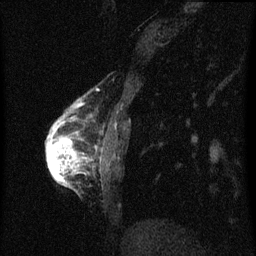
Breast MRI (dynamic contrast-enhanced), one sagittal slice. Position 13 of 60 along the scan axis. Dynamic contrast-enhanced series, image 2 of 3 at this slice position (ordered by acquisition). 1.5 T. TE 4.2 ms, TR 8 ms. 2 mm slice thickness. 256 × 256 image matrix, field of view 180 × 180 mm. Patient: female, 56 years.
Structures marked on this image (semi-automatic segmentation, software-assisted and operator-edited):
- analysis volume of interest (the breast-tissue region the enhancement analysis was run in; not a lesion): box from (x=46, y=114) to (x=89, y=183) px
- tumour enhancement mask (voxels above the 70 % enhancement threshold inside the analysis volume of interest): (x=48, y=124)–(x=79, y=183)